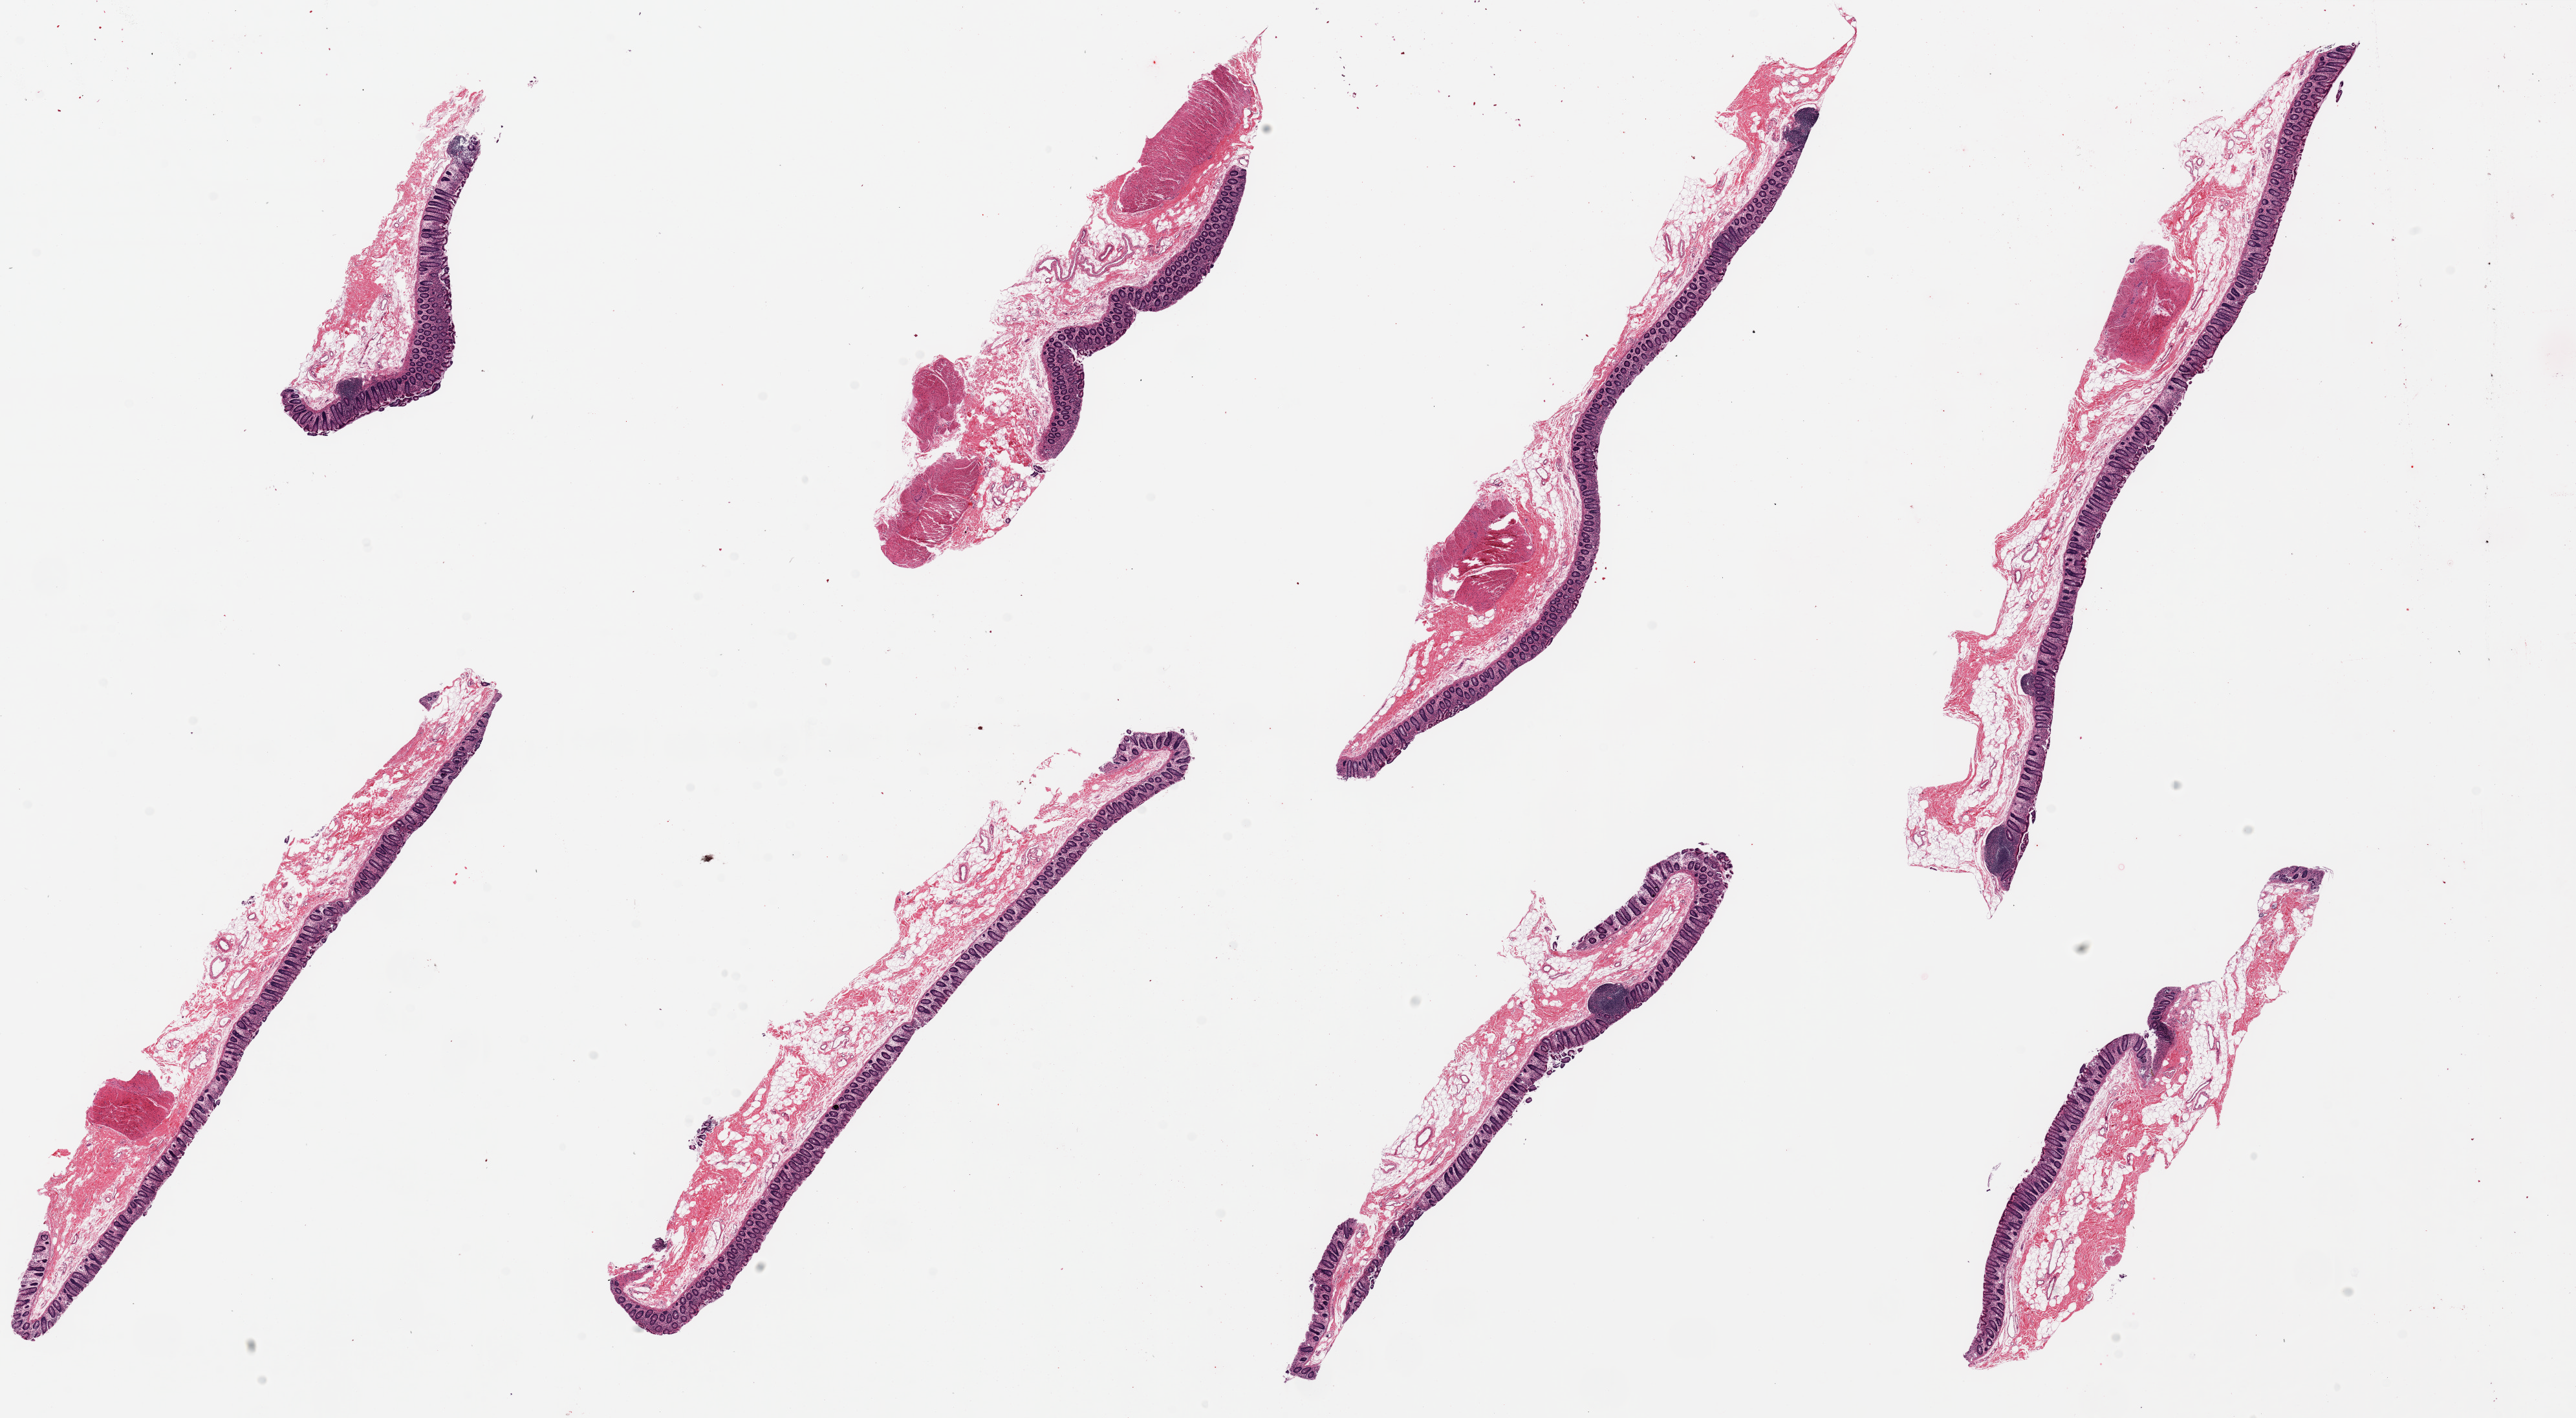
Whole-slide image, H&E stain, brightfield — shown as a low-resolution overview of the whole scanned area (about 31.5 x 17.3 mm). PAXgene-fixed paraffin-embedded (PFPE) section. Target tissue: transverse colon. Donor tissue sample.
Reviewer comment on this tissue sample: 8 pieces ~10x1mm, Mucosa moderate well preserved, ~20-25% of thickness; some areas starting to degrade to autolysis score2.